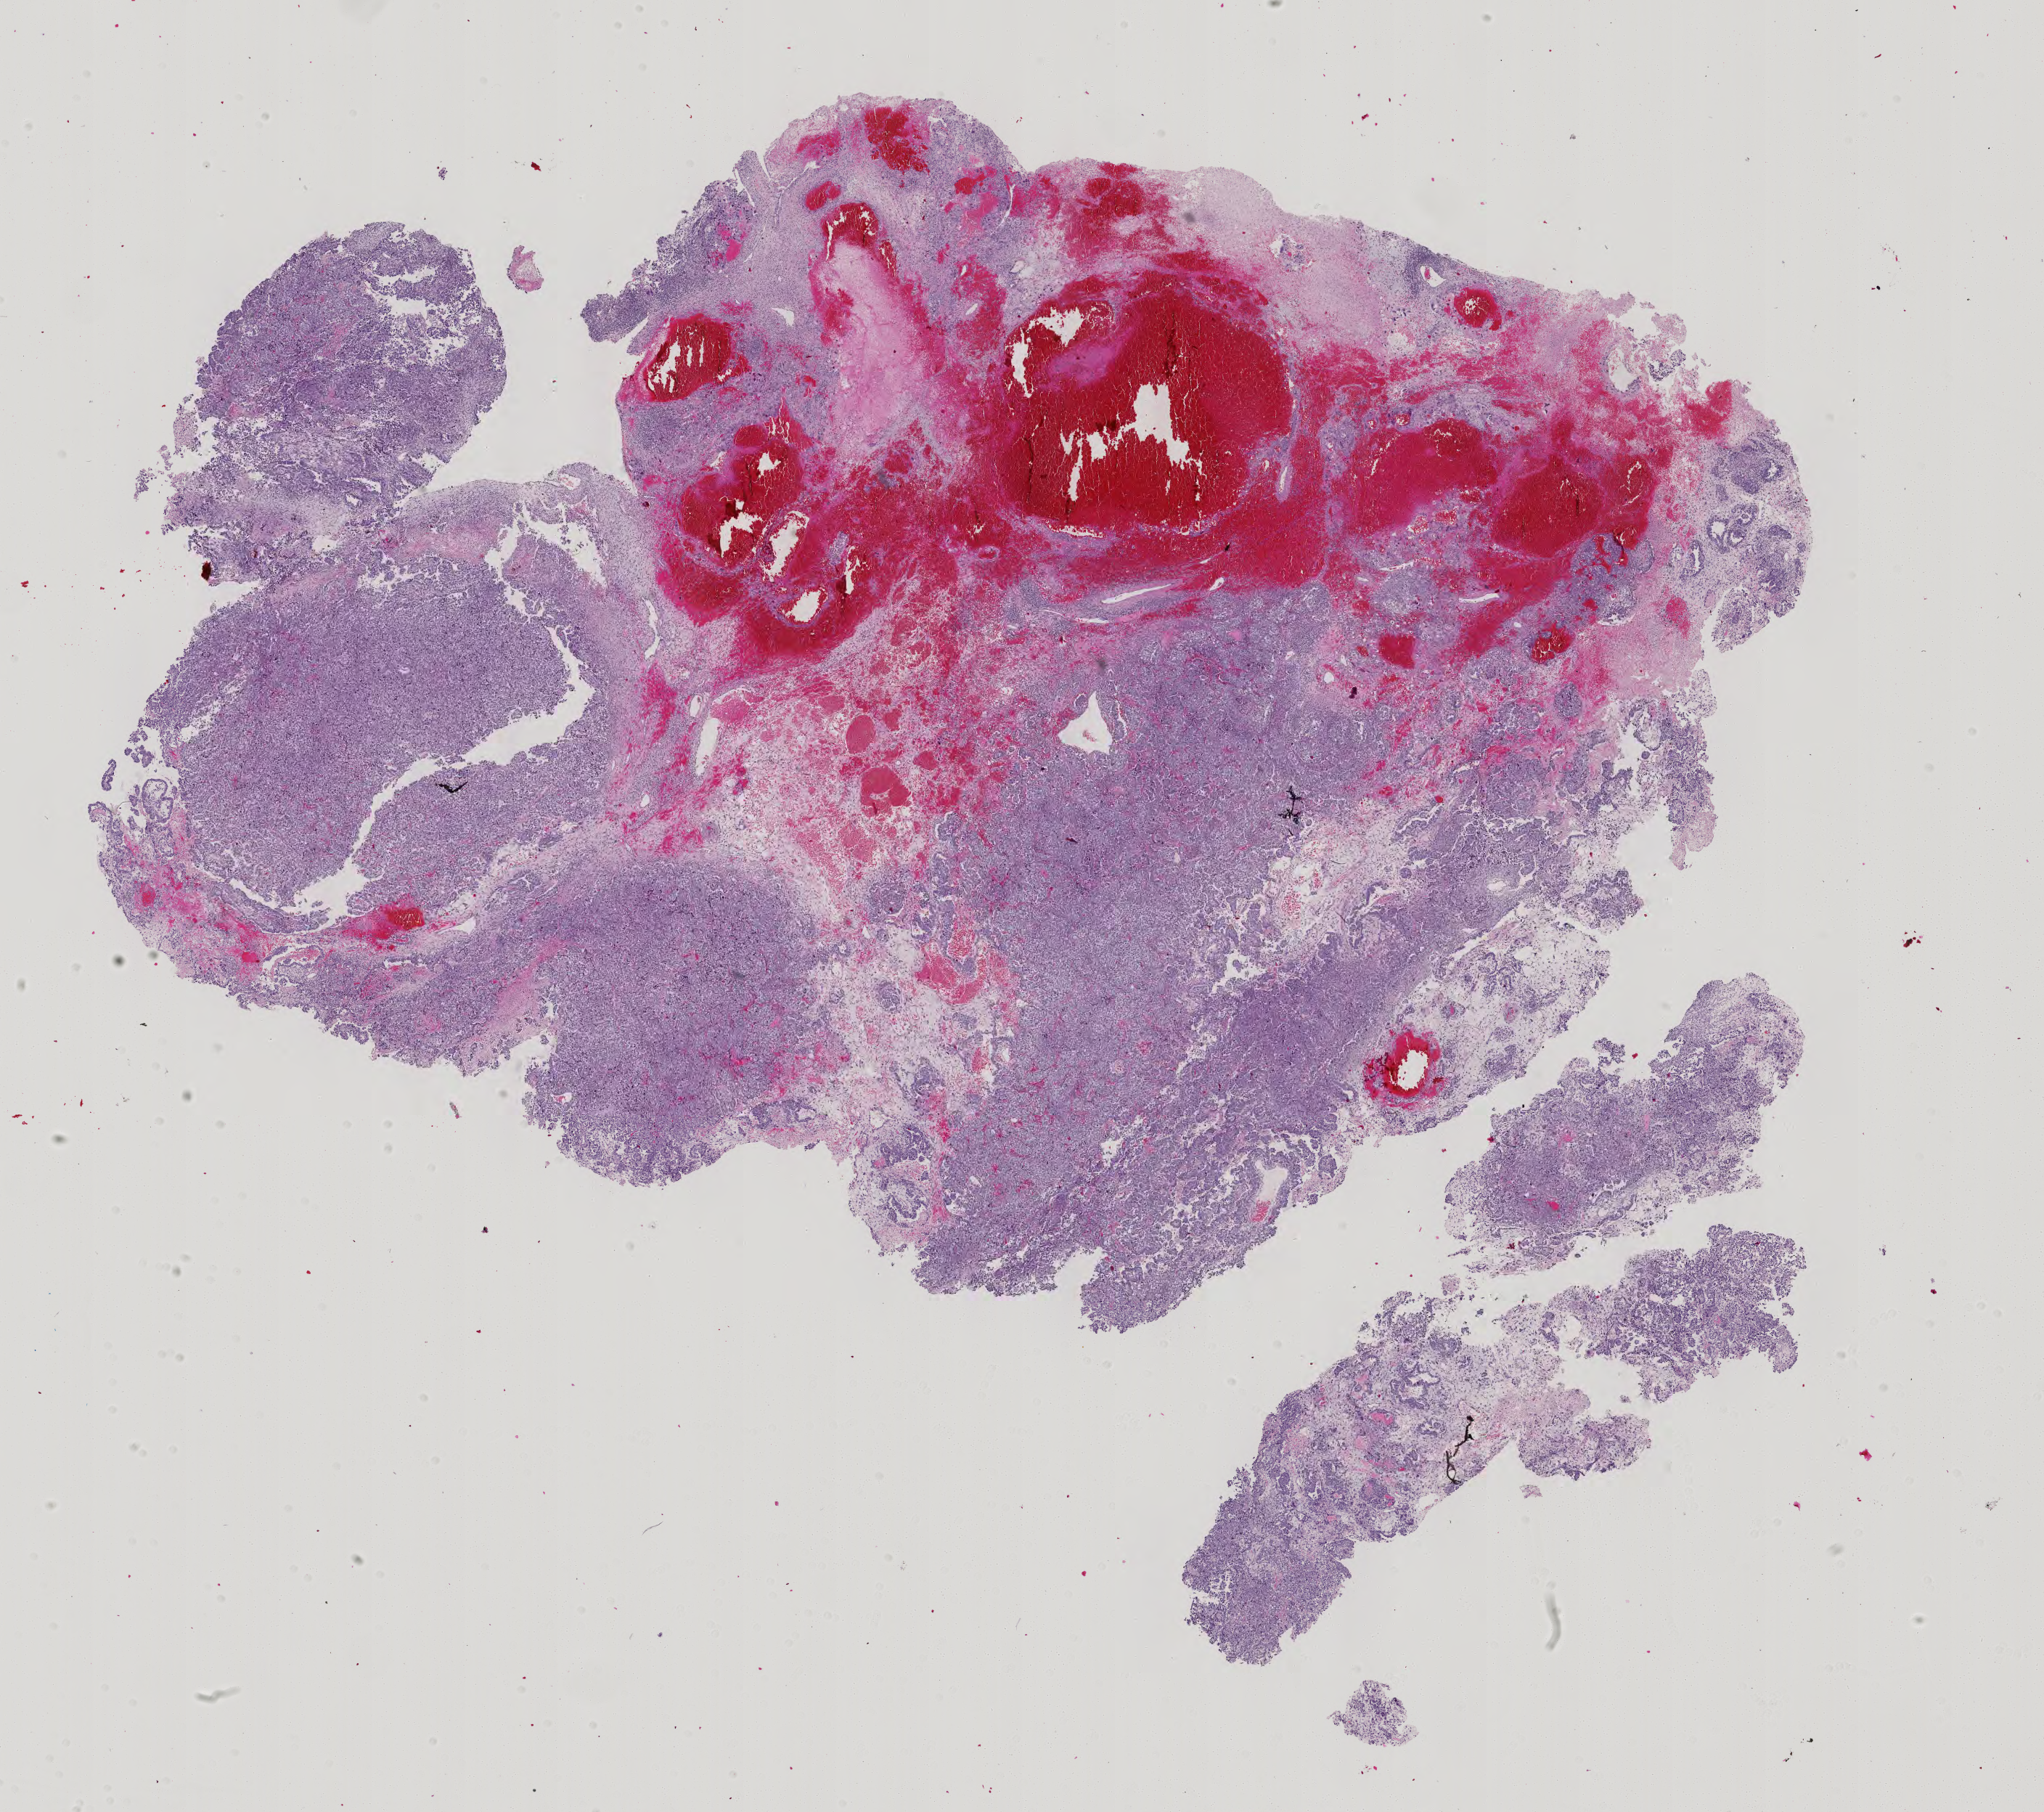
H&E whole-slide image — low-resolution overview of the scanned area, about 20.5 x 18.2 mm (slide scanned at 40x), FFPE section, primary tumour sample from the testis. Male, age 41 years at initial diagnosis.
Histologic diagnosis: Embryonal carcinoma, NOS.